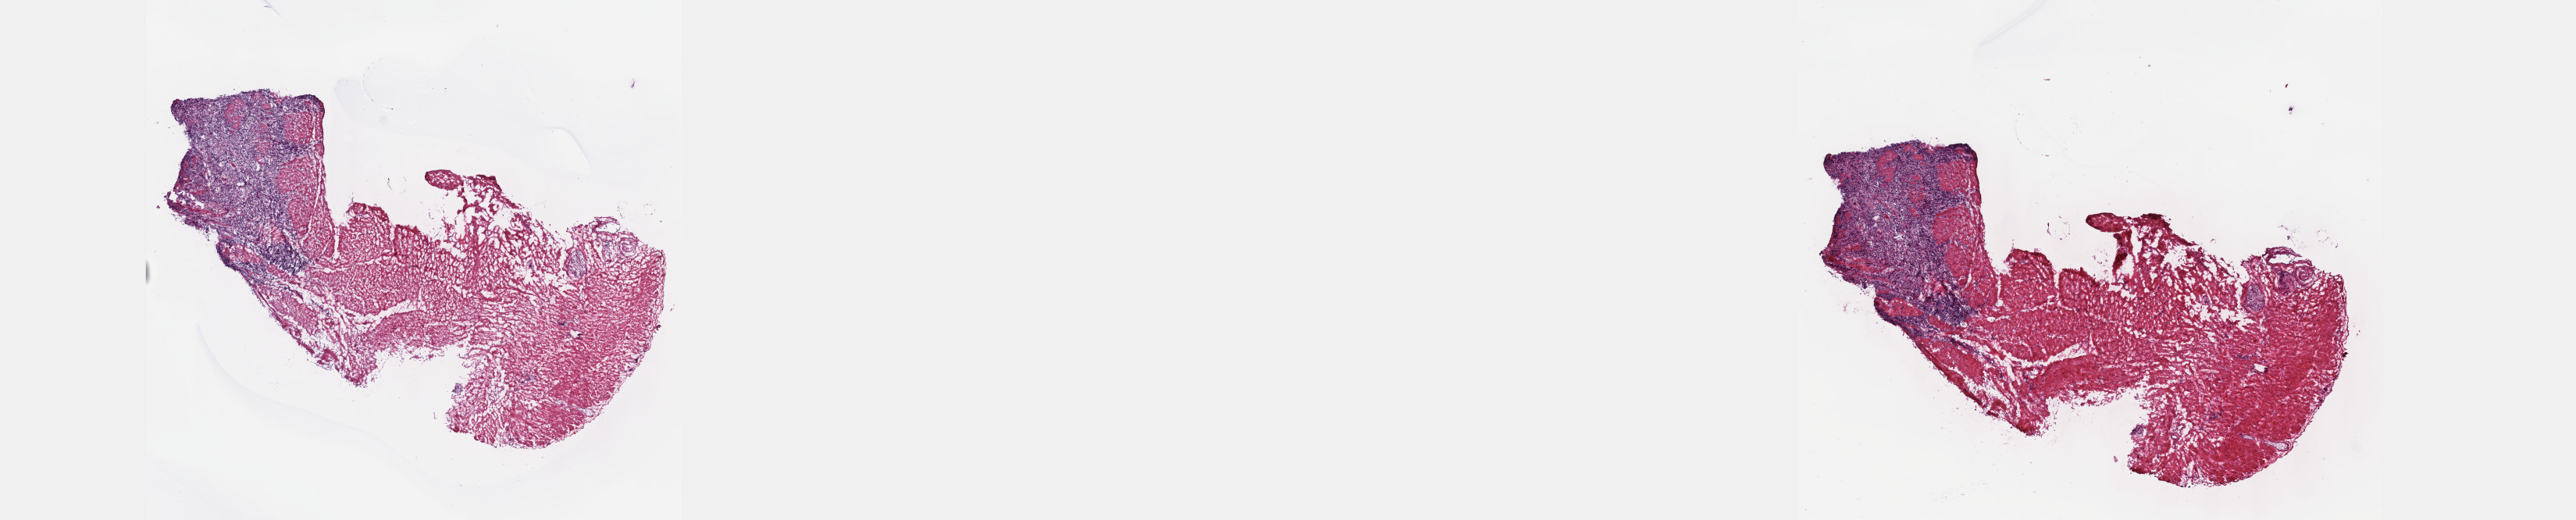
Whole-slide histology image, H&E-stained — shown as a low-resolution overview of the whole scanned area (about 26.7 x 5.4 mm, acquisition: 40x scan); frozen section from the top of the tissue portion; stomach, primary tumour sample. Patient: male, age at initial diagnosis 57 years. Histologic grade: GX (grade cannot be assessed). Composition of this section per pathologist review: tumour cells 15%, tumour nuclei 75%, normal cells 0%, stromal cells 84%, necrosis 1%. Inflammatory infiltration, as recorded: lymphocyte infiltration 12%, monocyte infiltration 1%, neutrophil infiltration 1%.
- diagnosis: Signet ring cell carcinoma (body of stomach)